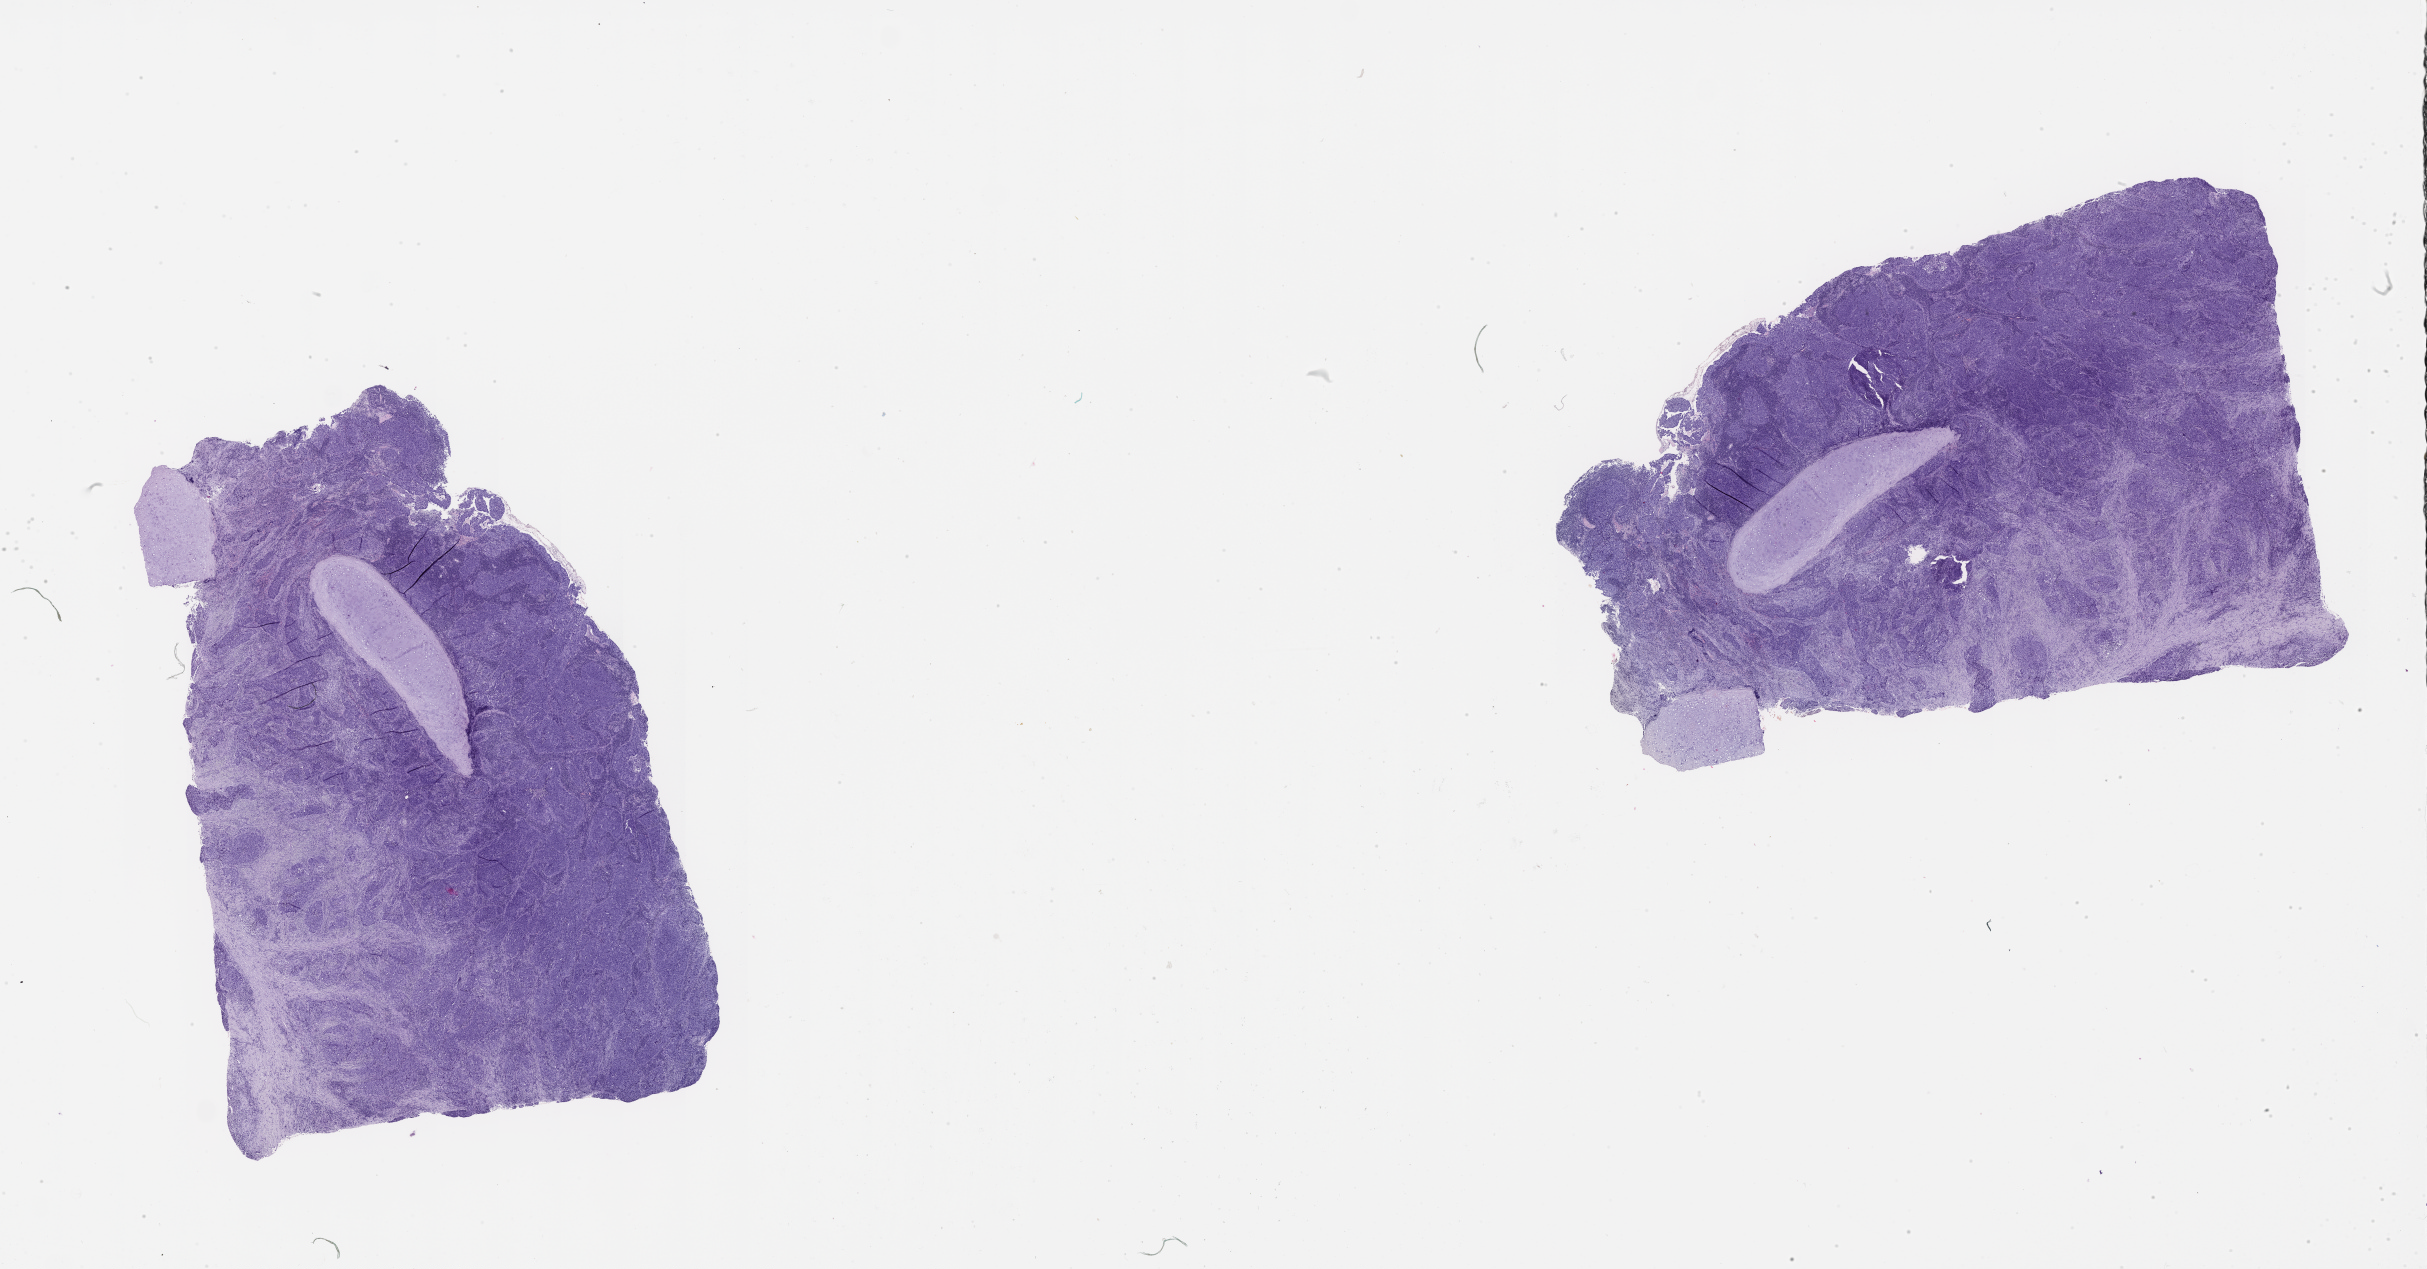
H&E-stained whole-slide image — whole scanned area (about 39.1 x 20.4 mm) shown as a low-resolution overview. Lung, tumour tissue. 63-year-old male patient.
Patient diagnosis (cohort enrolment): squamous cell carcinoma (lung).